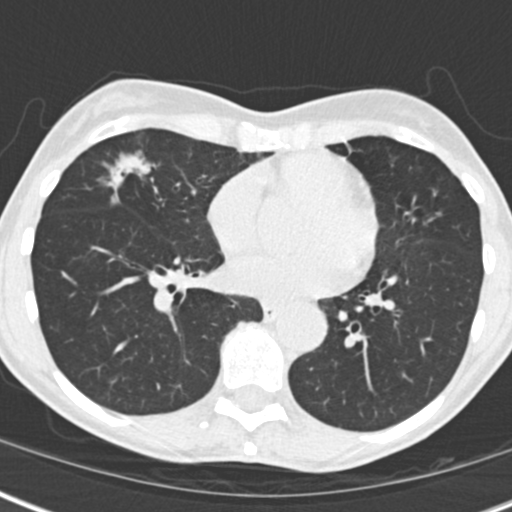
Low-dose screening chest CT, one axial slice. Position 72 of 173 along the scan axis. 120 kVp. Lung window (W 1500 / L -600 HU). 2 mm slice thickness. 512 × 512 image matrix, field of view 290 × 290 mm.
Outlined on this slice (outlined manually by an expert reader):
- lesion 1 (tumor, middle lobe of right lung): bounding box [x1, y1, x2, y2] px = [111, 156, 149, 185]